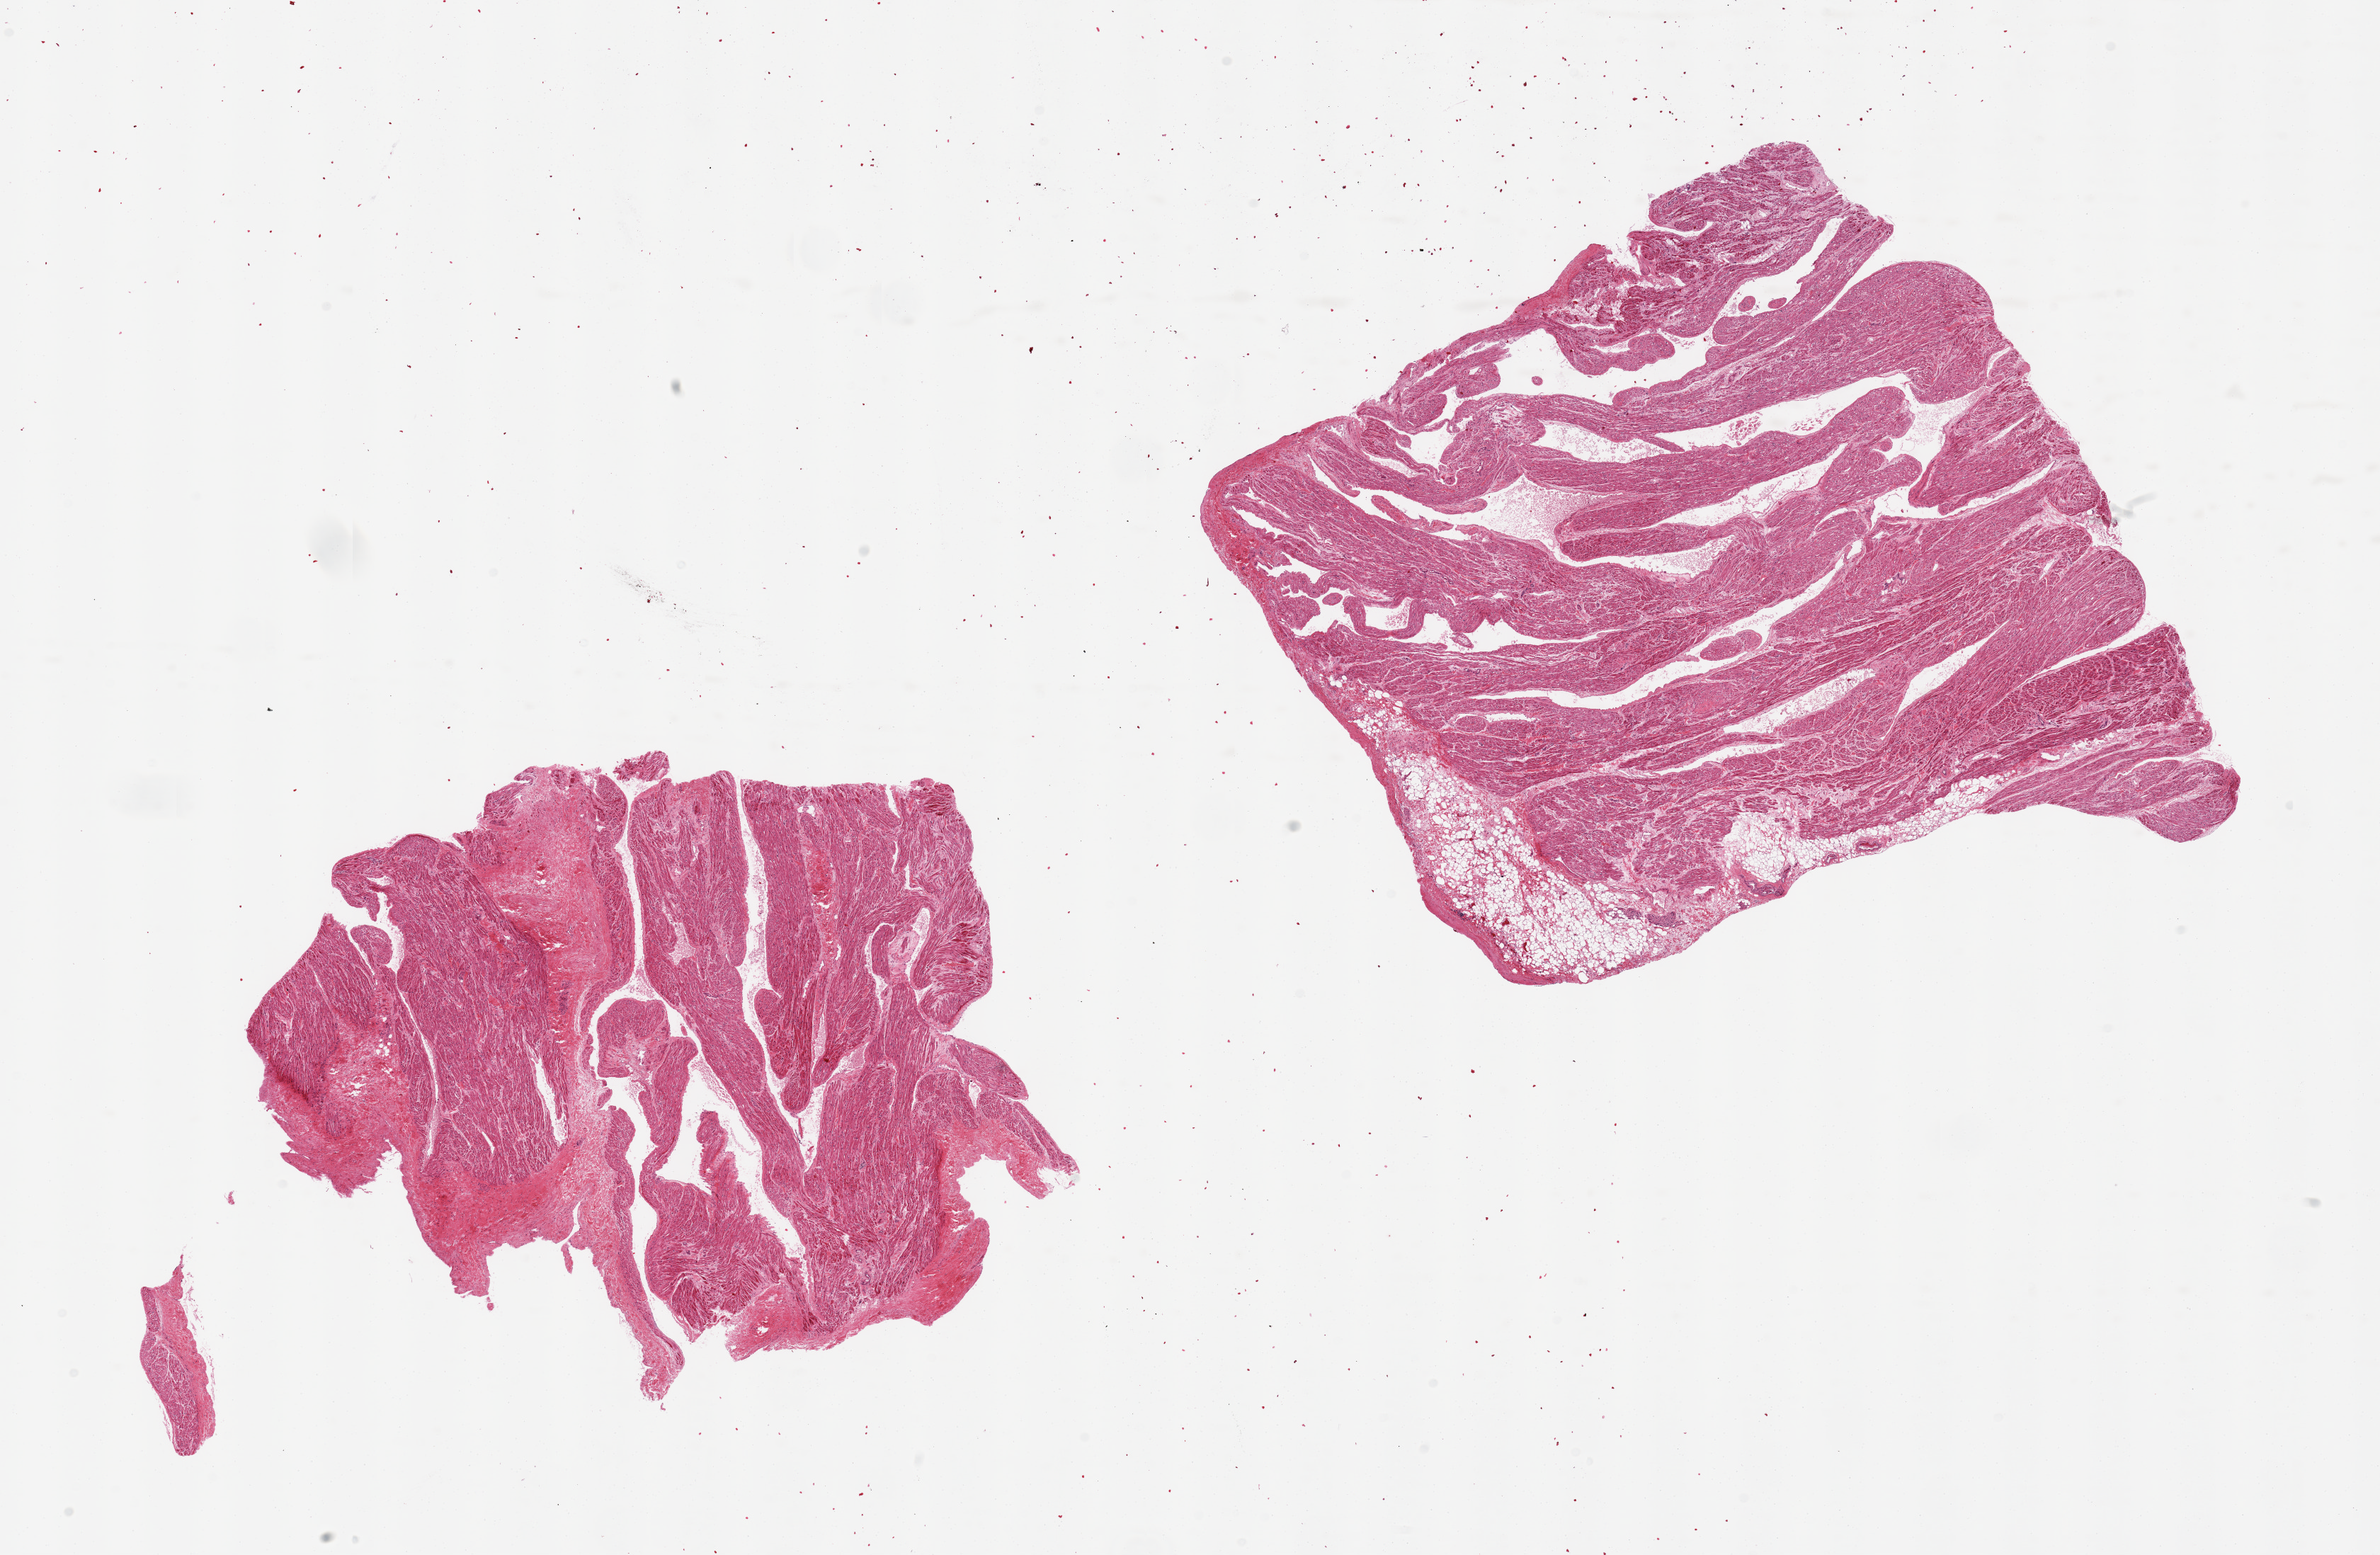
Digitized haematoxylin and eosin-stained section, a low-resolution overview of the entire scanned area, about 26.6 x 17.4 mm. PAXgene-fixed paraffin-embedded (PFPE) section. Target tissue: auricular appendage. Tissue donor sample. Donor sex: male.
Pathologist's review note for this sample: 2 pieces, larger piece includes up to ~10% fat.